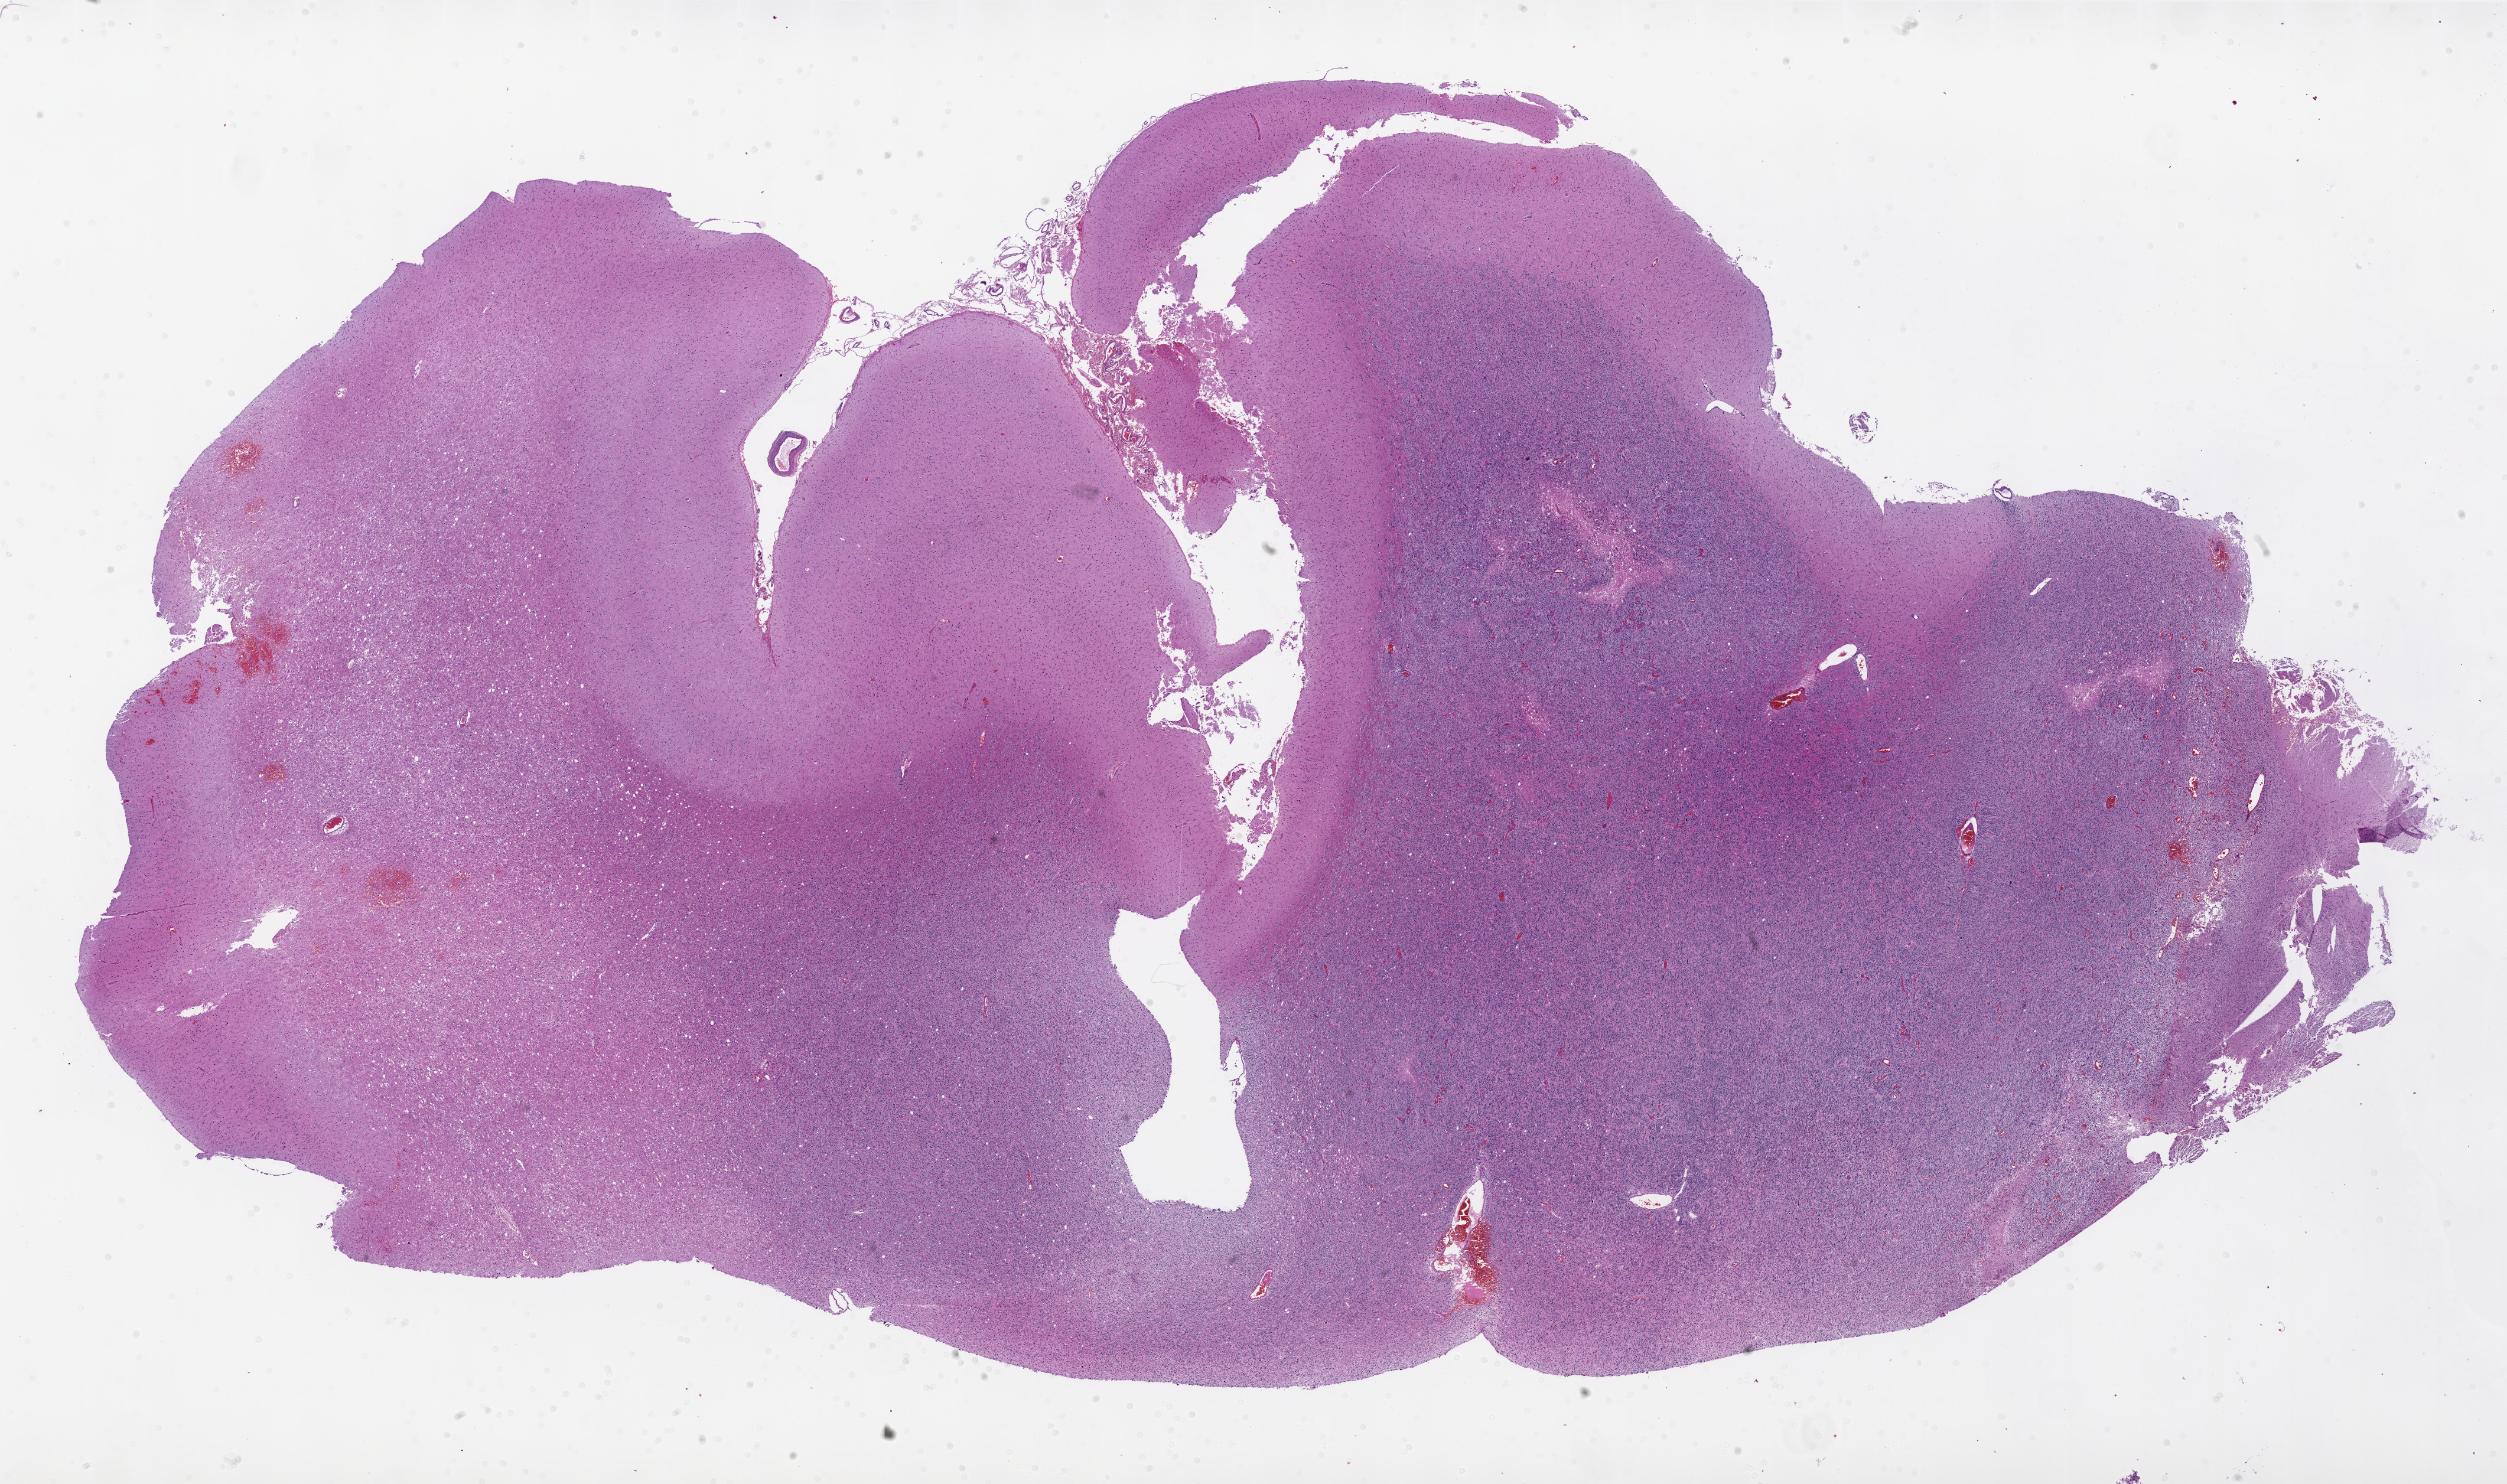
H&E whole-slide image, a low-resolution overview of the entire scanned area, about 34.0 x 20.1 mm (slide scanned at 20x), formalin-fixed paraffin-embedded (FFPE) diagnostic section, sample: primary tumour, brain. Patient: male, age at initial diagnosis 49 years.
• pathologic diagnosis: Glioblastoma